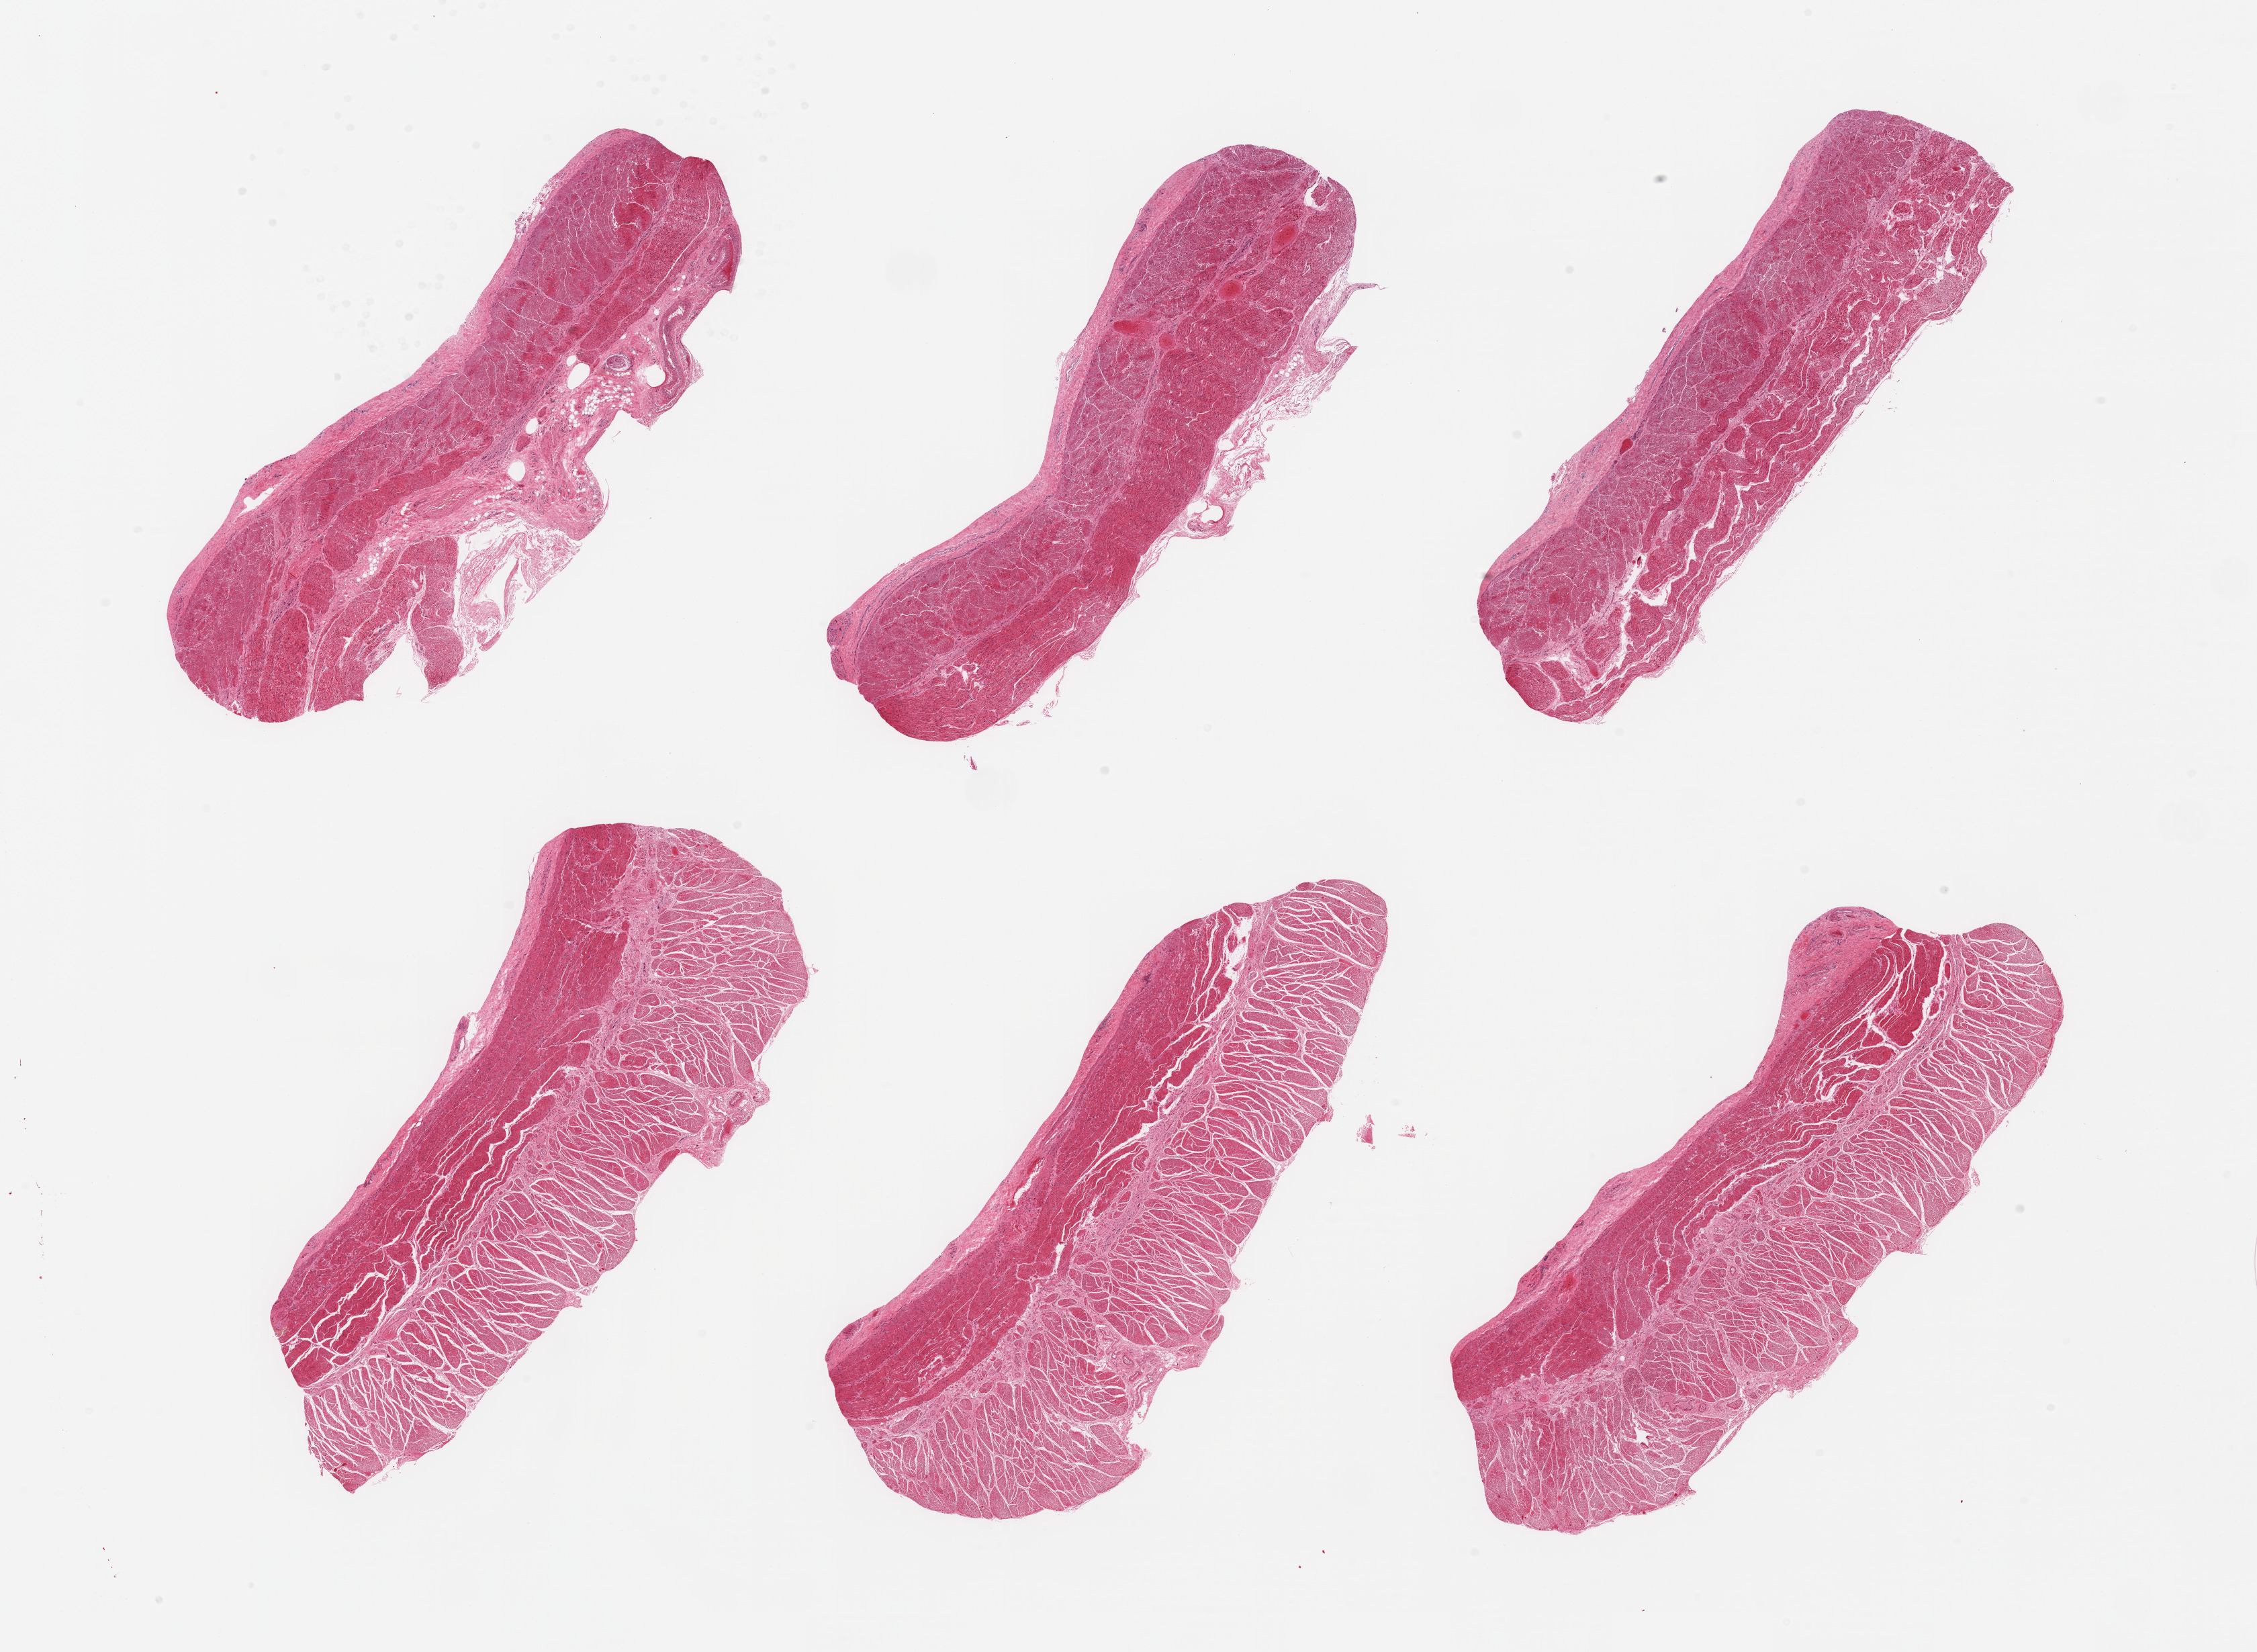
Digitized haematoxylin and eosin-stained section — whole scanned area (about 26.6 x 19.5 mm) shown as a low-resolution overview, PAXgene-fixed paraffin-embedded (PFPE) section, section of esophageal muscle (target tissue), tissue donor sample. Donor sex: male.
Reviewer comment on this tissue sample: 6 pieces; well dissected.